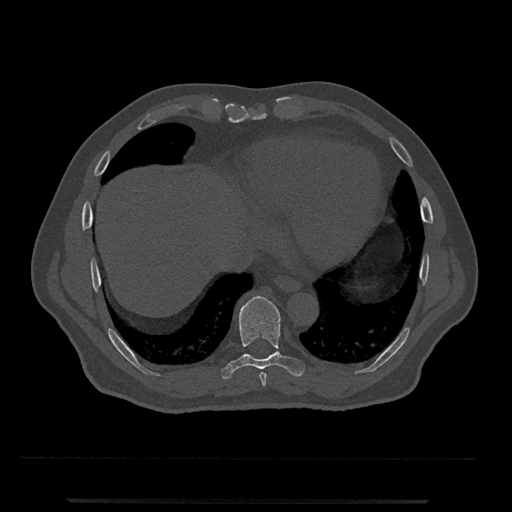
CT including the spine, one axial slice; slice 576 of 797 in the series (ordered by position); bone window (W 1800 / L 400 HU); 0.5 mm slice thickness; 512 × 512 image matrix, field of view 419 × 419 mm. Male patient, age 63 years. From the clinical record (not read from this slice): primary cancer: prostate.
Structures marked on this image (semi-automatically segmented with operator editing):
- T8 vertebra: bounding box <259,372,267,387> (left, top, right, bottom; pixels)
- T9 vertebra: <221,296,305,379>